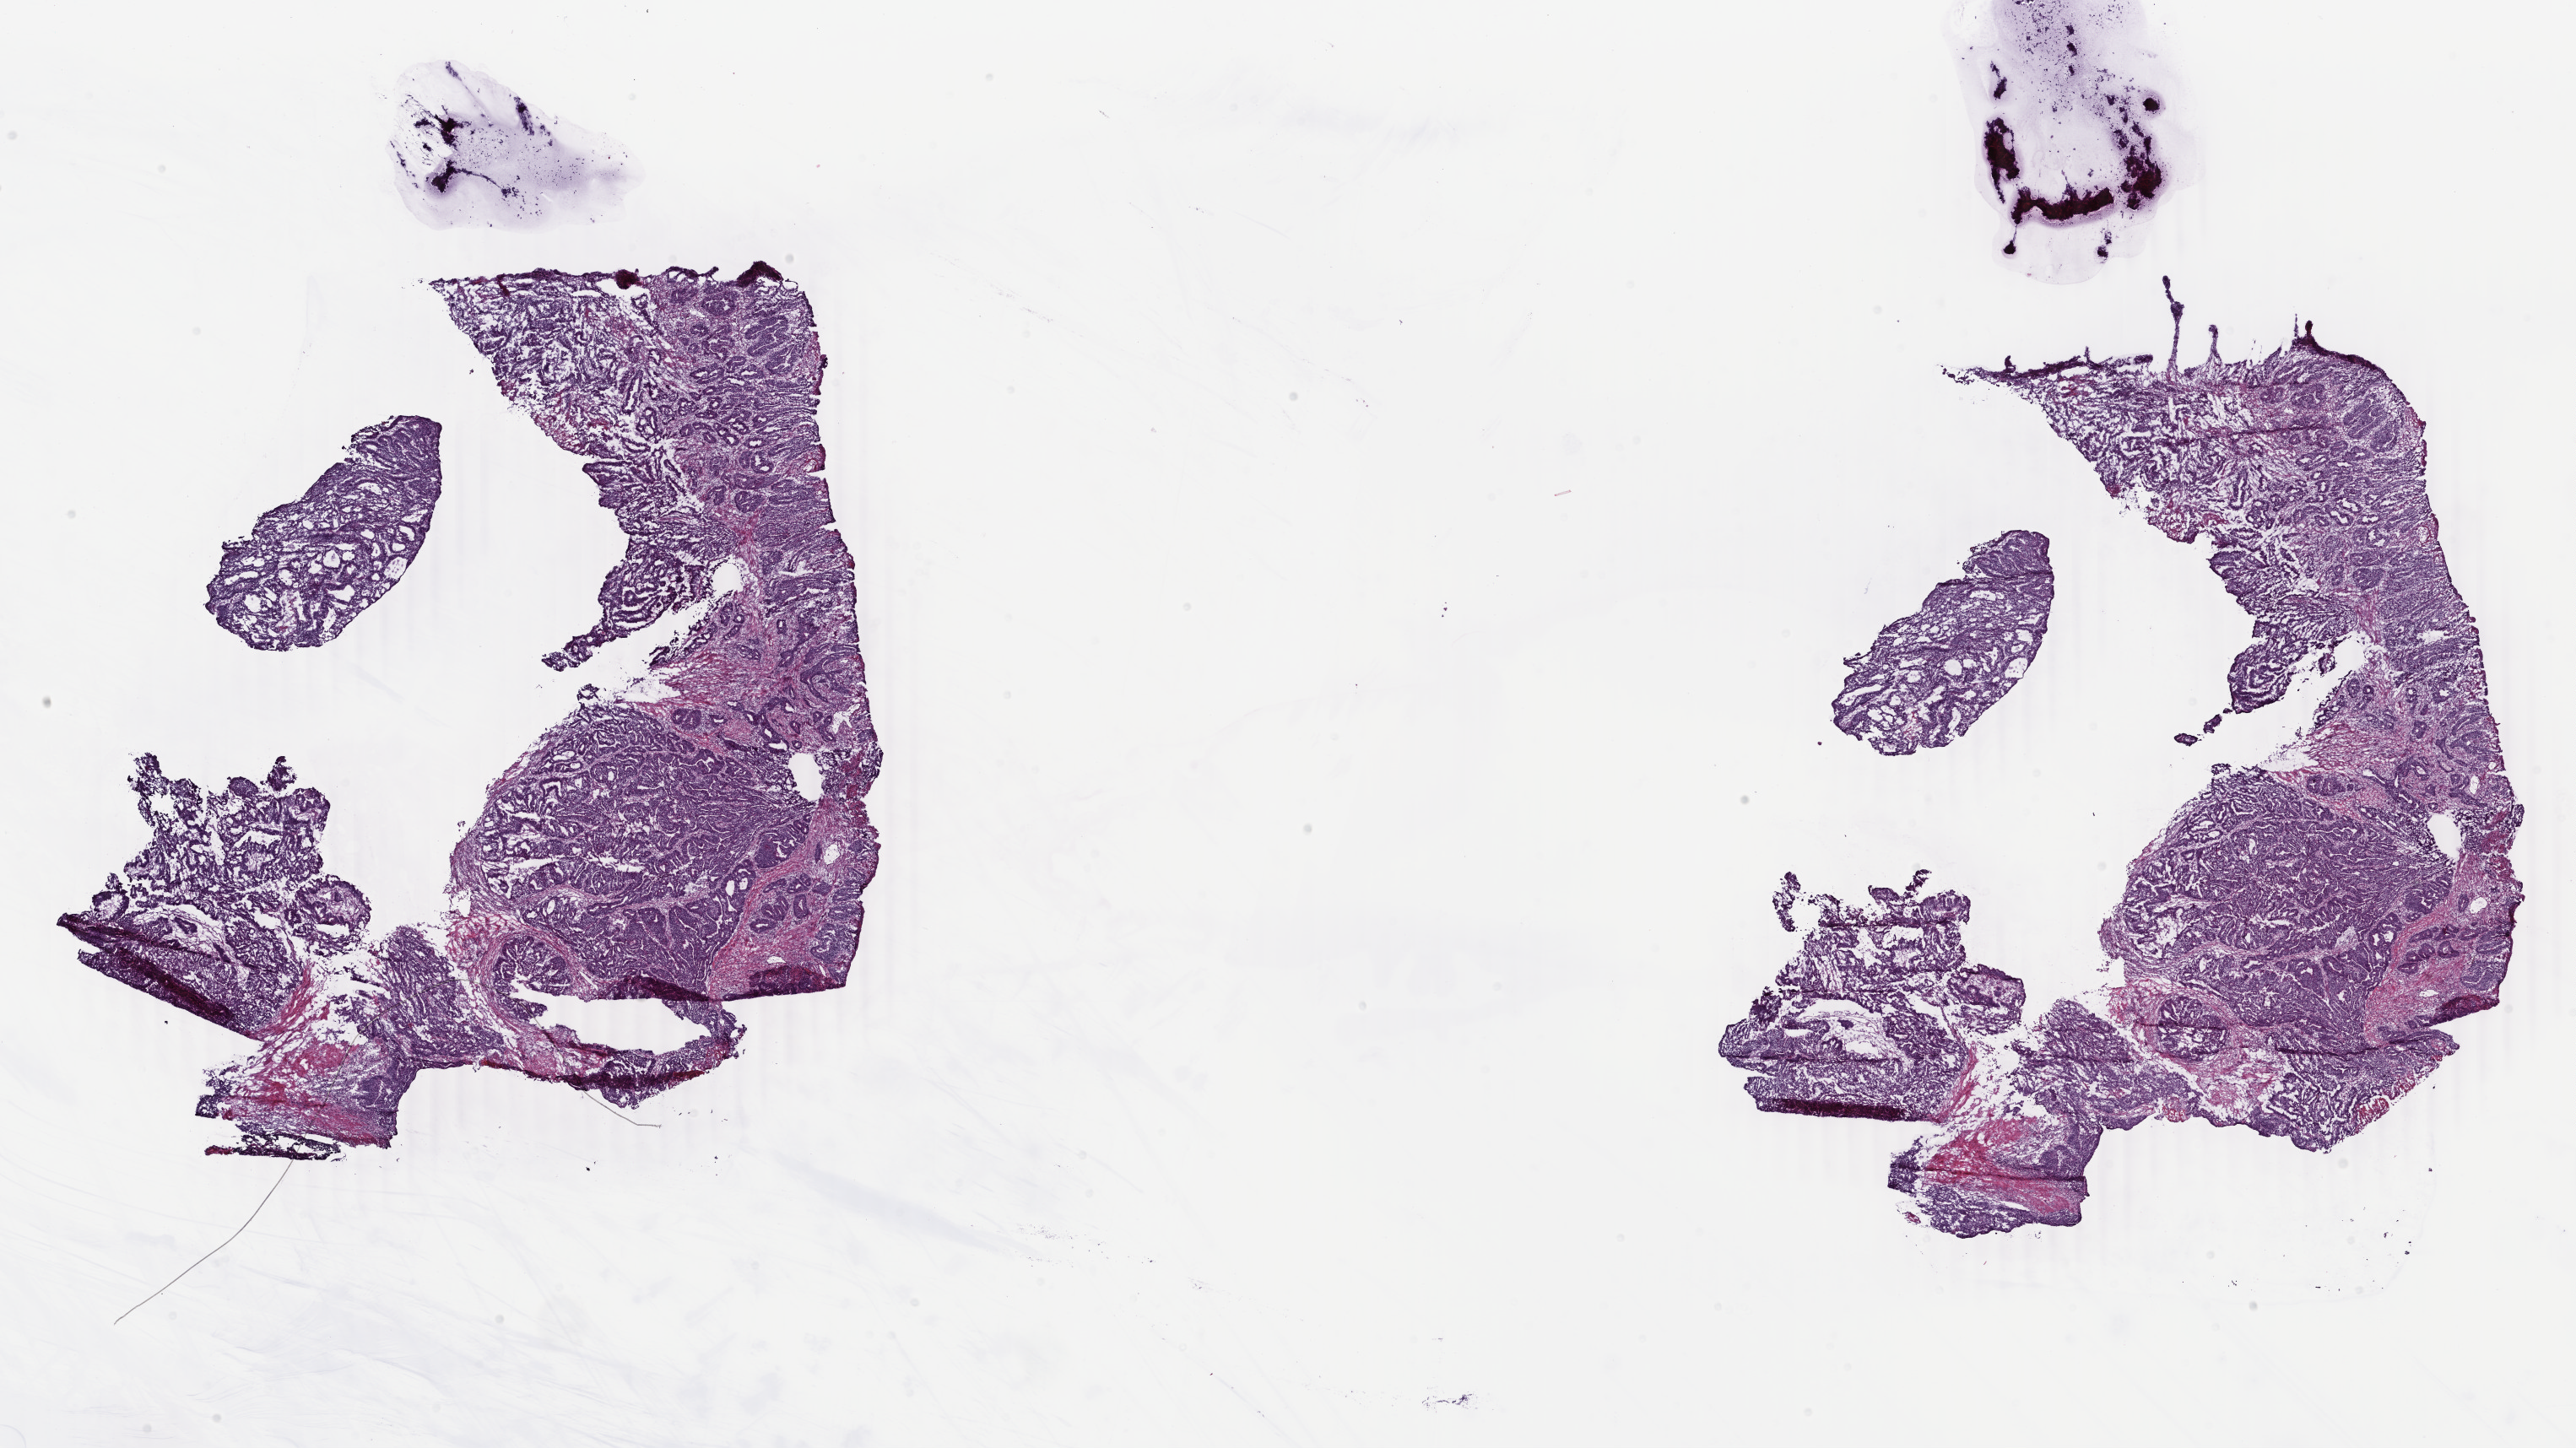
Whole-slide histology image, H&E — low-resolution overview of the scanned area, about 24.3 x 13.6 mm (slide scanned at 40x), frozen section from the top of the tissue portion, rectum, primary tumour sample. Male, age 71 years at initial diagnosis. Composition of this section per pathologist review: tumour cells 85%, tumour nuclei 85%.
Diagnosis: Adenocarcinoma, NOS.